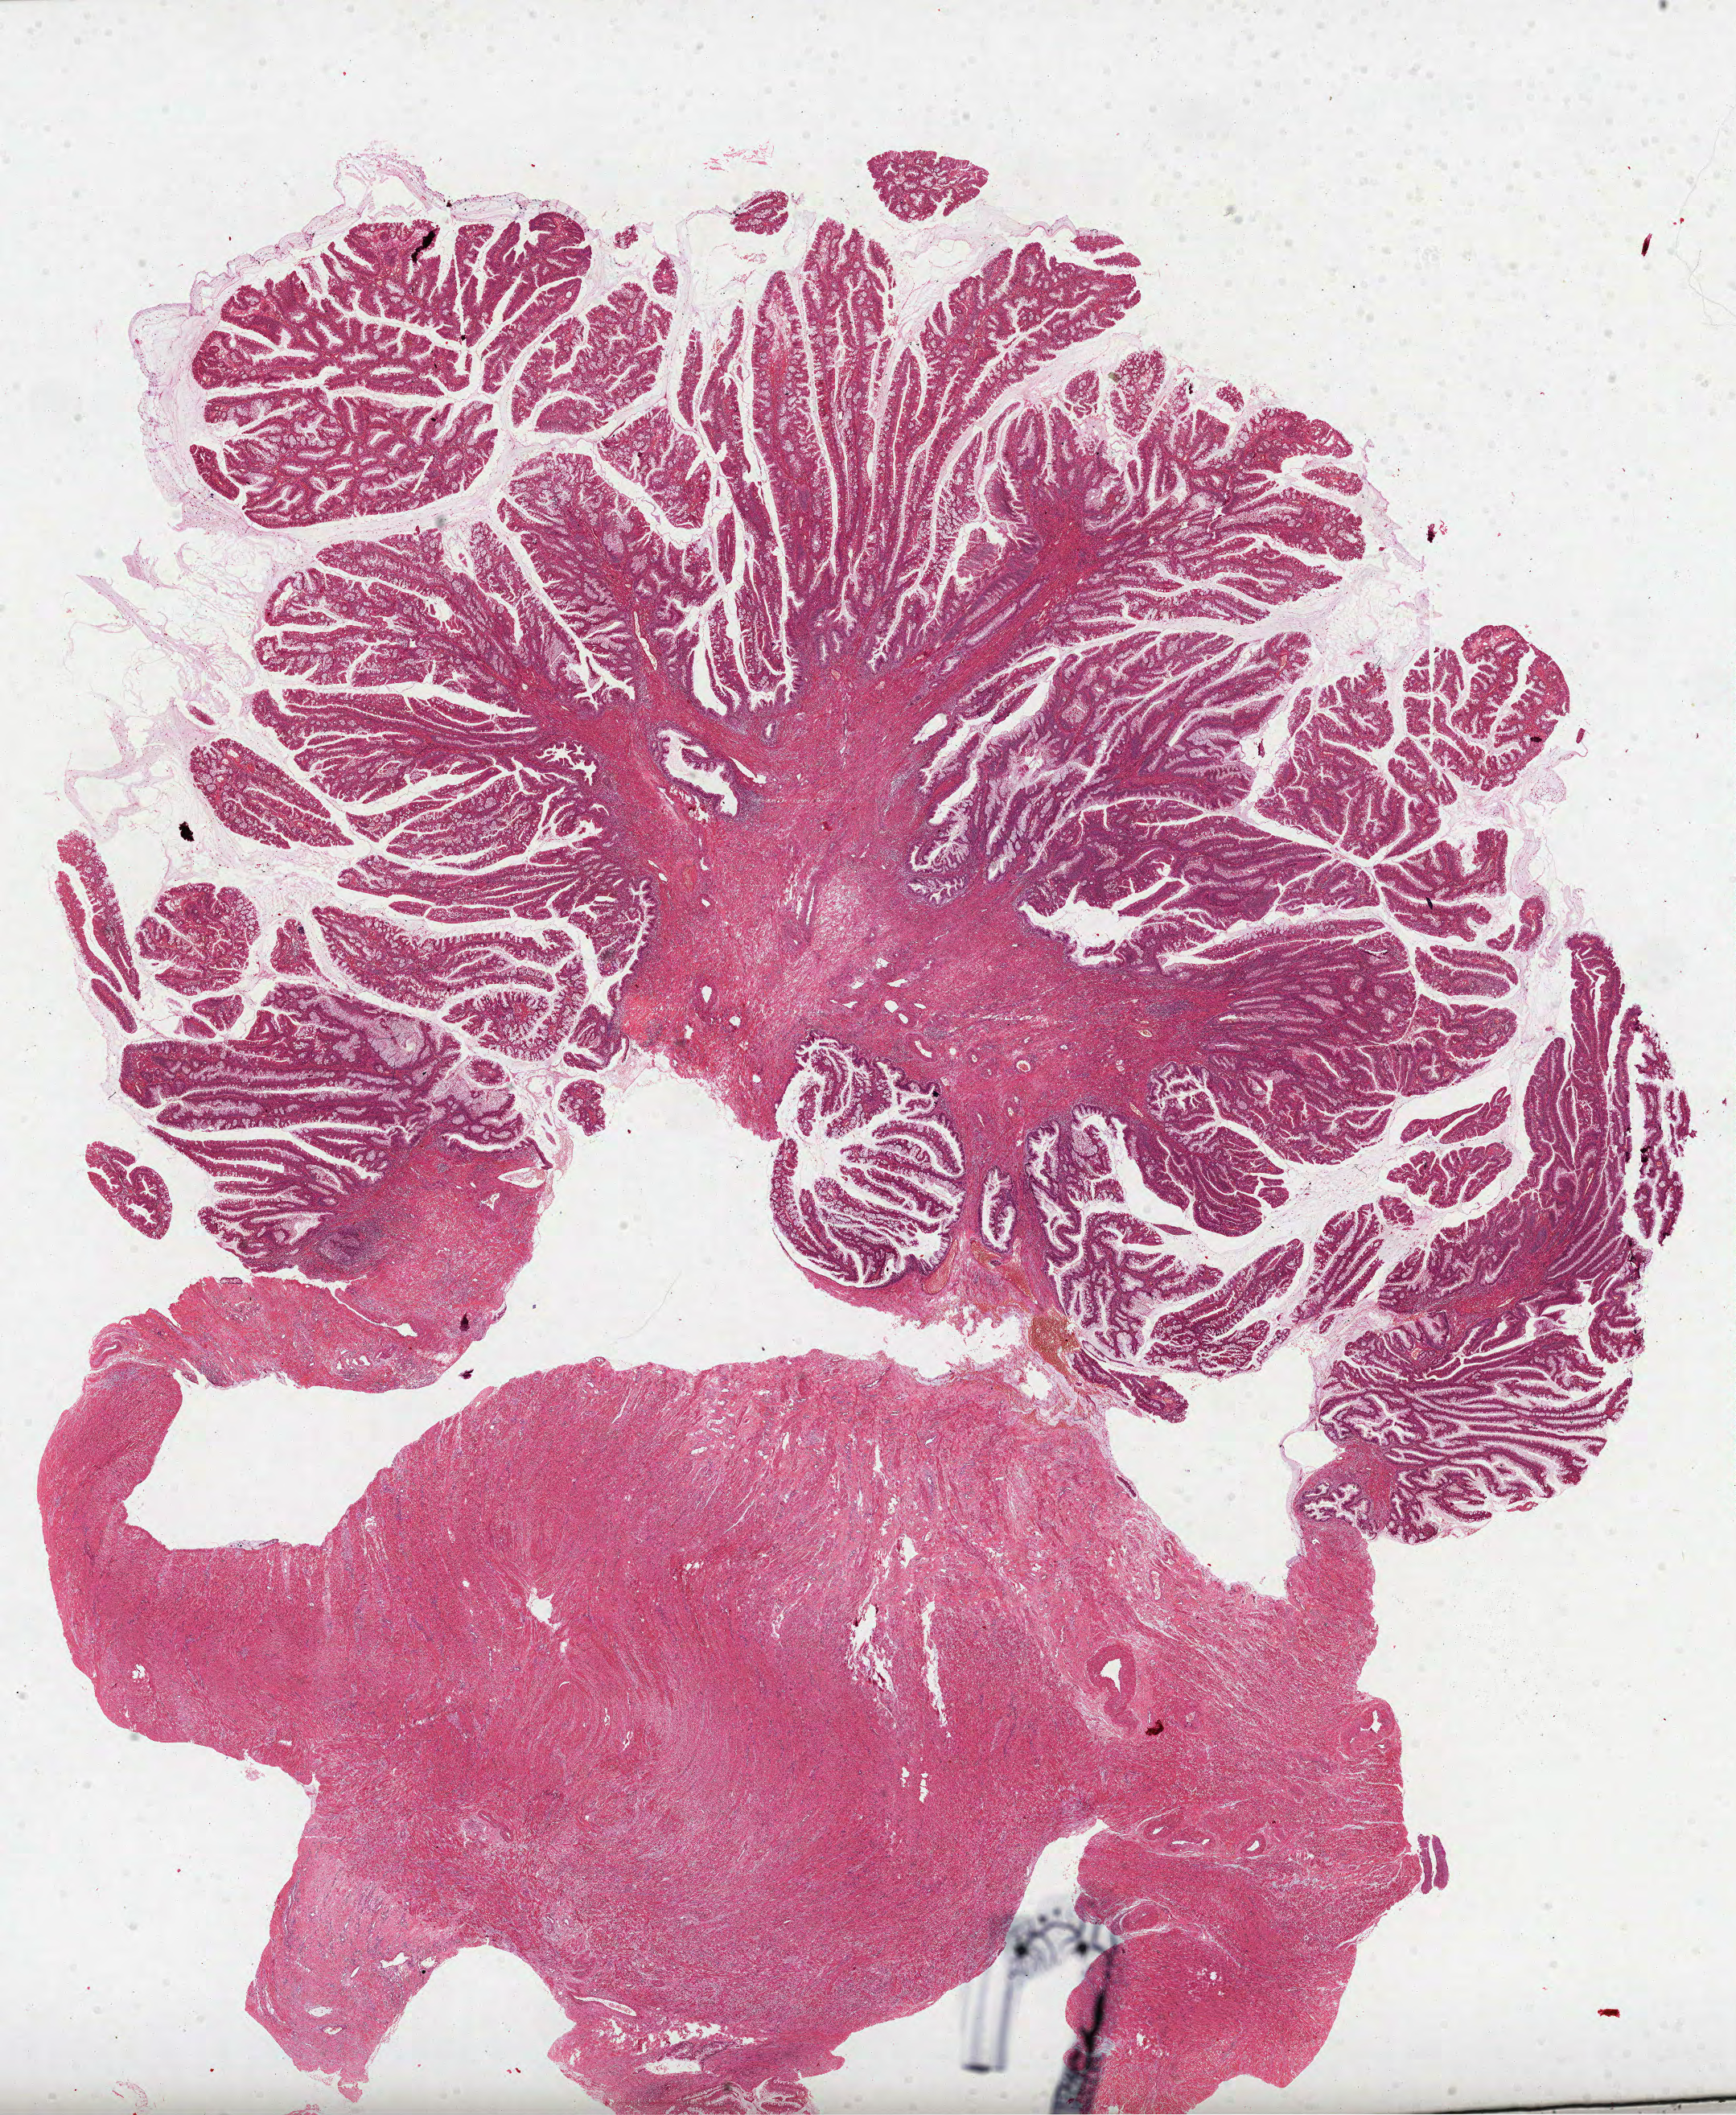
Hematoxylin and eosin (H&E) stained whole-slide image — whole scanned area (about 17.4 x 21.2 mm) shown as a low-resolution overview. Formalin-fixed paraffin-embedded (FFPE) diagnostic section. Colon, primary tumour sample. Female, age 52 years at initial diagnosis.
AJCC pathologic stage: IIA (6th edition). Diagnosis: Mucinous adenocarcinoma (ascending colon).